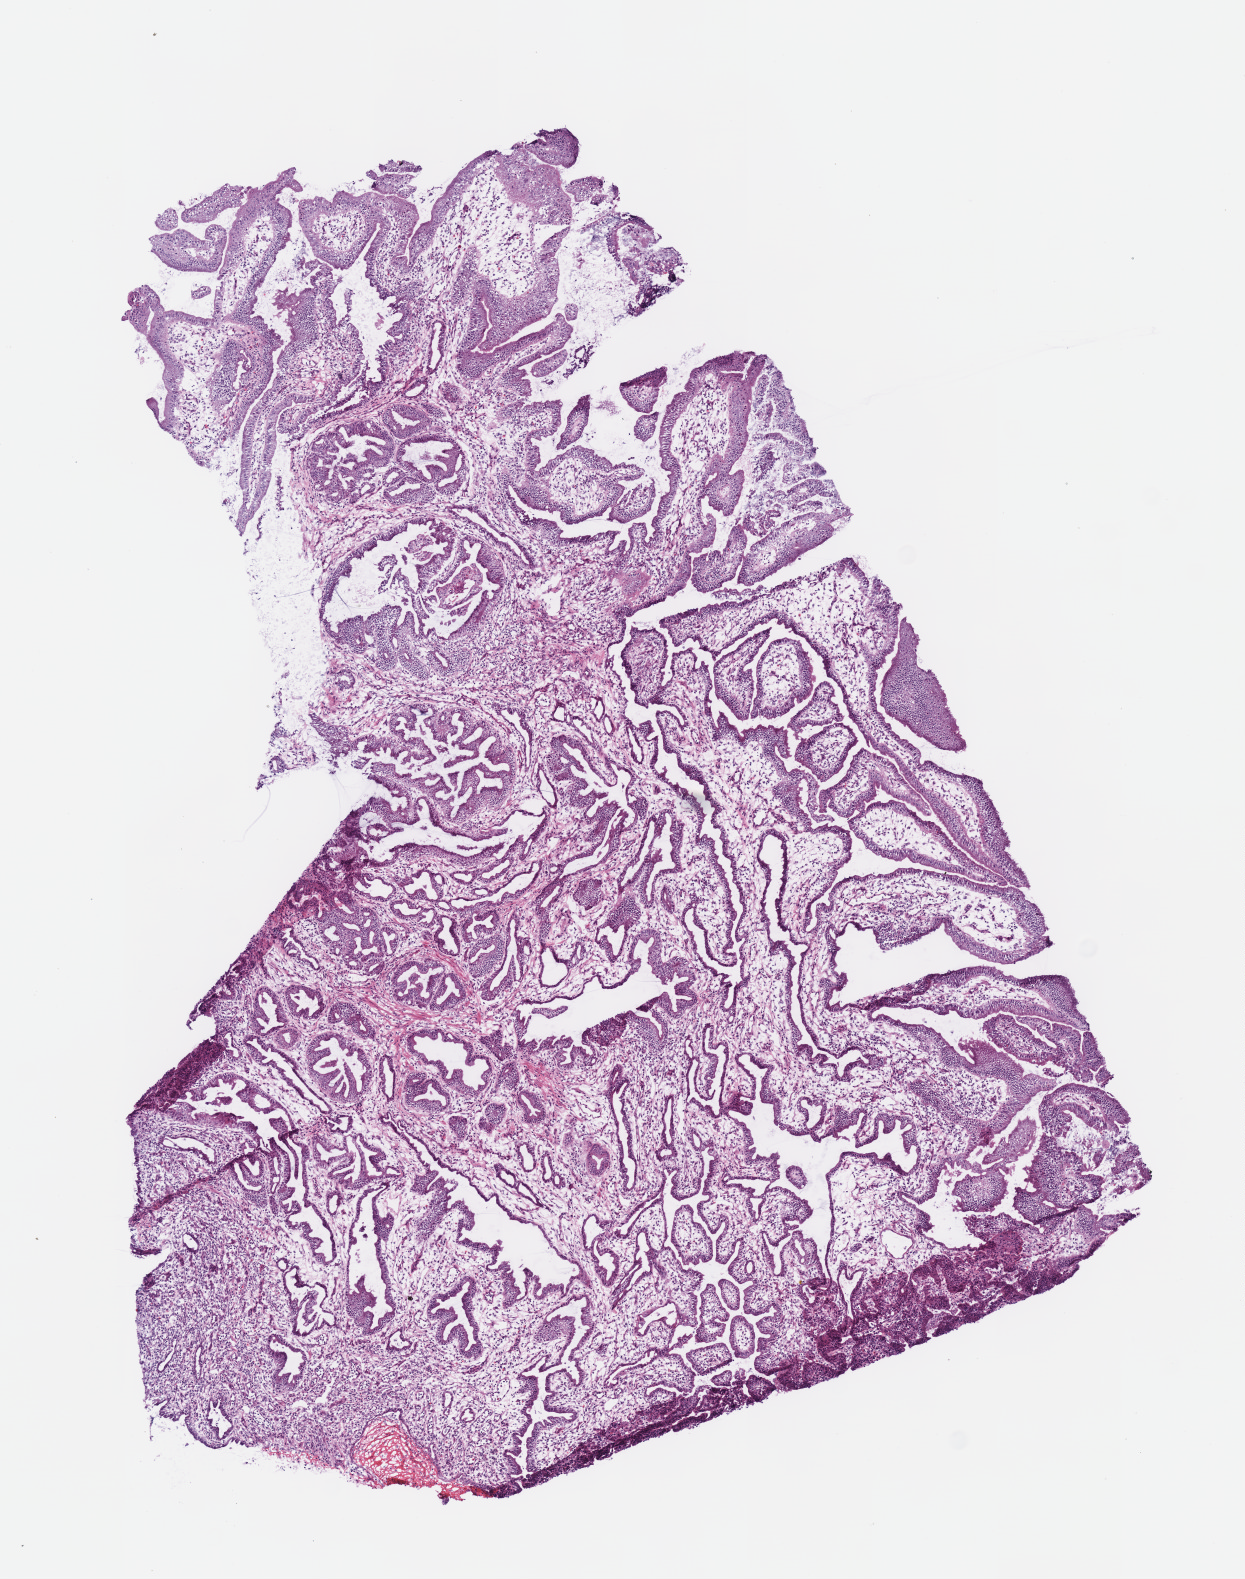
Digitized H&E tissue section (whole slide) — a low-resolution overview of the entire scanned area, about 4.9 x 6.2 mm (slide scanned at 40x). Frozen section from the top of the tissue portion. Primary tumour sample from the pancreas. Female, age 84 years at initial diagnosis. Pathologist review of this section (percent, as recorded): tumour cells 100%, tumour nuclei 80%.
Diagnosis: Mucinous adenocarcinoma (head of pancreas).